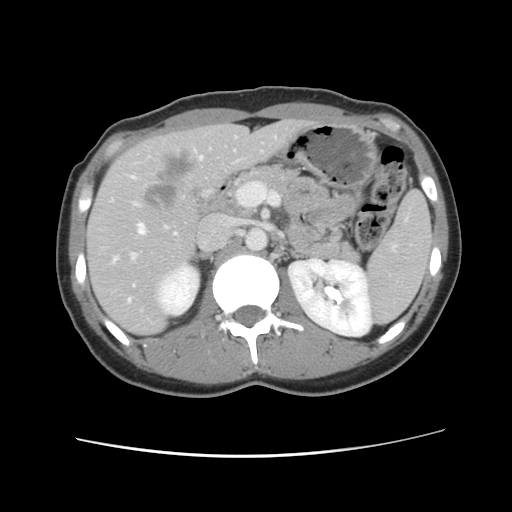
Contrast-enhanced abdominal CT, one axial slice. 120 kVp. Intravenous contrast given. Soft-tissue window (W 400 / L 40 HU). 2.5 mm slice thickness. 512 × 512 image matrix, field of view 339 × 339 mm. Female patient, age 33 years. From the clinical record (not read from this slice): diagnosis: colorectal cancer liver metastases, imaged before liver resection; multiple liver metastases: yes; largest metastasis: 4.5 cm.
Structures marked on this image (outlined manually by an expert reader):
- hepatic veins: bounding box (x1, y1, x2, y2) in pixels: (113, 157, 203, 302)
- liver: (89, 120, 312, 334)
- planned liver remnant (the part of the liver to remain after resection): (89, 120, 311, 334)
- portal vein (with intrahepatic branches): (129, 224, 178, 262)
- liver metastasis: (142, 152, 196, 214)